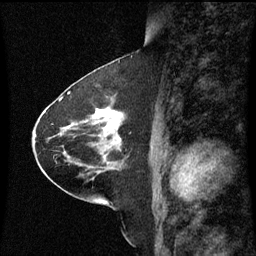
Breast MRI (dynamic contrast-enhanced), one sagittal slice. Slice 33 of 60 in the series (ordered by position). Dynamic contrast-enhanced series, image 2 of 3 at this slice position (ordered by acquisition). 1.5 T. TE 4.2 ms, TR 8.9 ms. 2 mm slice thickness. 256 × 256 image matrix, field of view 200 × 200 mm. Female patient, age 63 years. Case-level facts recorded for this patient, not image findings: setting: breast cancer imaged before/during neoadjuvant chemotherapy; receptor status: HR-positive, HER2-negative.
Annotated regions visible in this slice (semi-automatic segmentation, software-assisted and operator-edited):
- analysis volume of interest (the breast-tissue region the enhancement analysis was run in; not a lesion): box from (x=77, y=100) to (x=127, y=151) px
- tumour enhancement mask (voxels above the 70 % enhancement threshold inside the analysis volume of interest): (x=95, y=108)–(x=120, y=141)